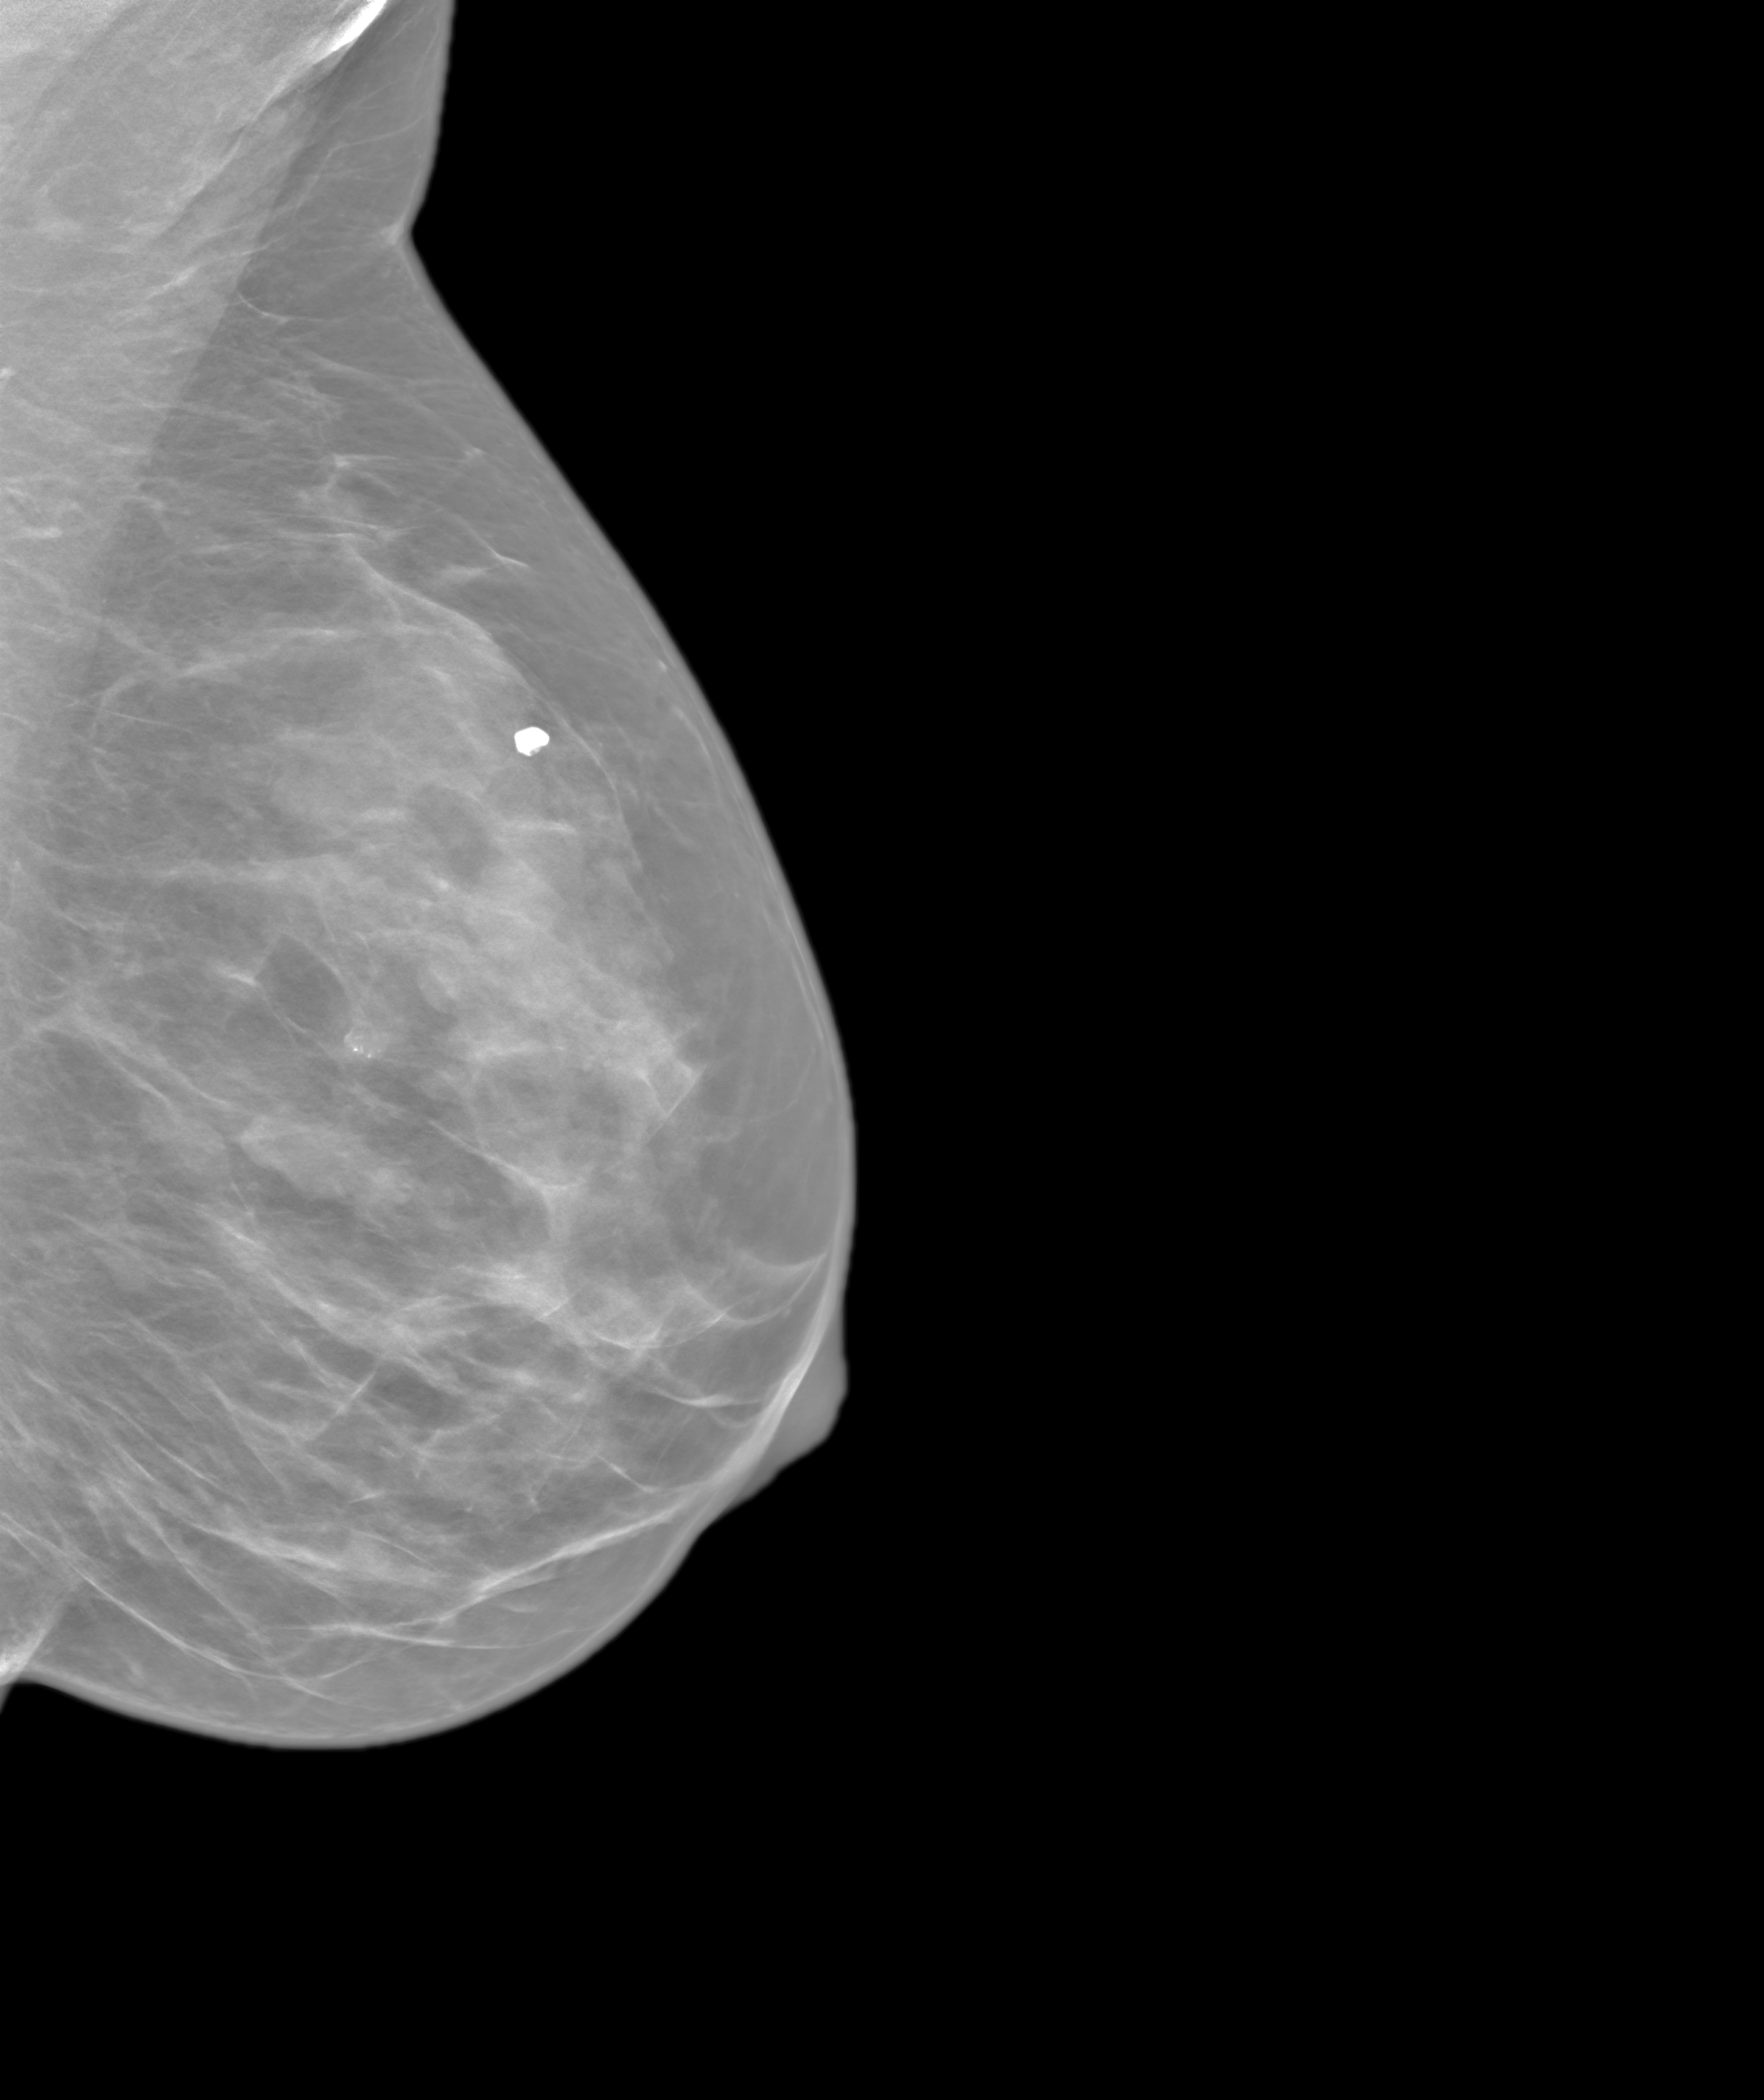
Annual screening mammography examination, system: SenoIris_1SP2(440). Patient aged 52 years (female).
Image type: synthesized 2-D view from tomosynthesis. Breast: left. Projection: MLO view.